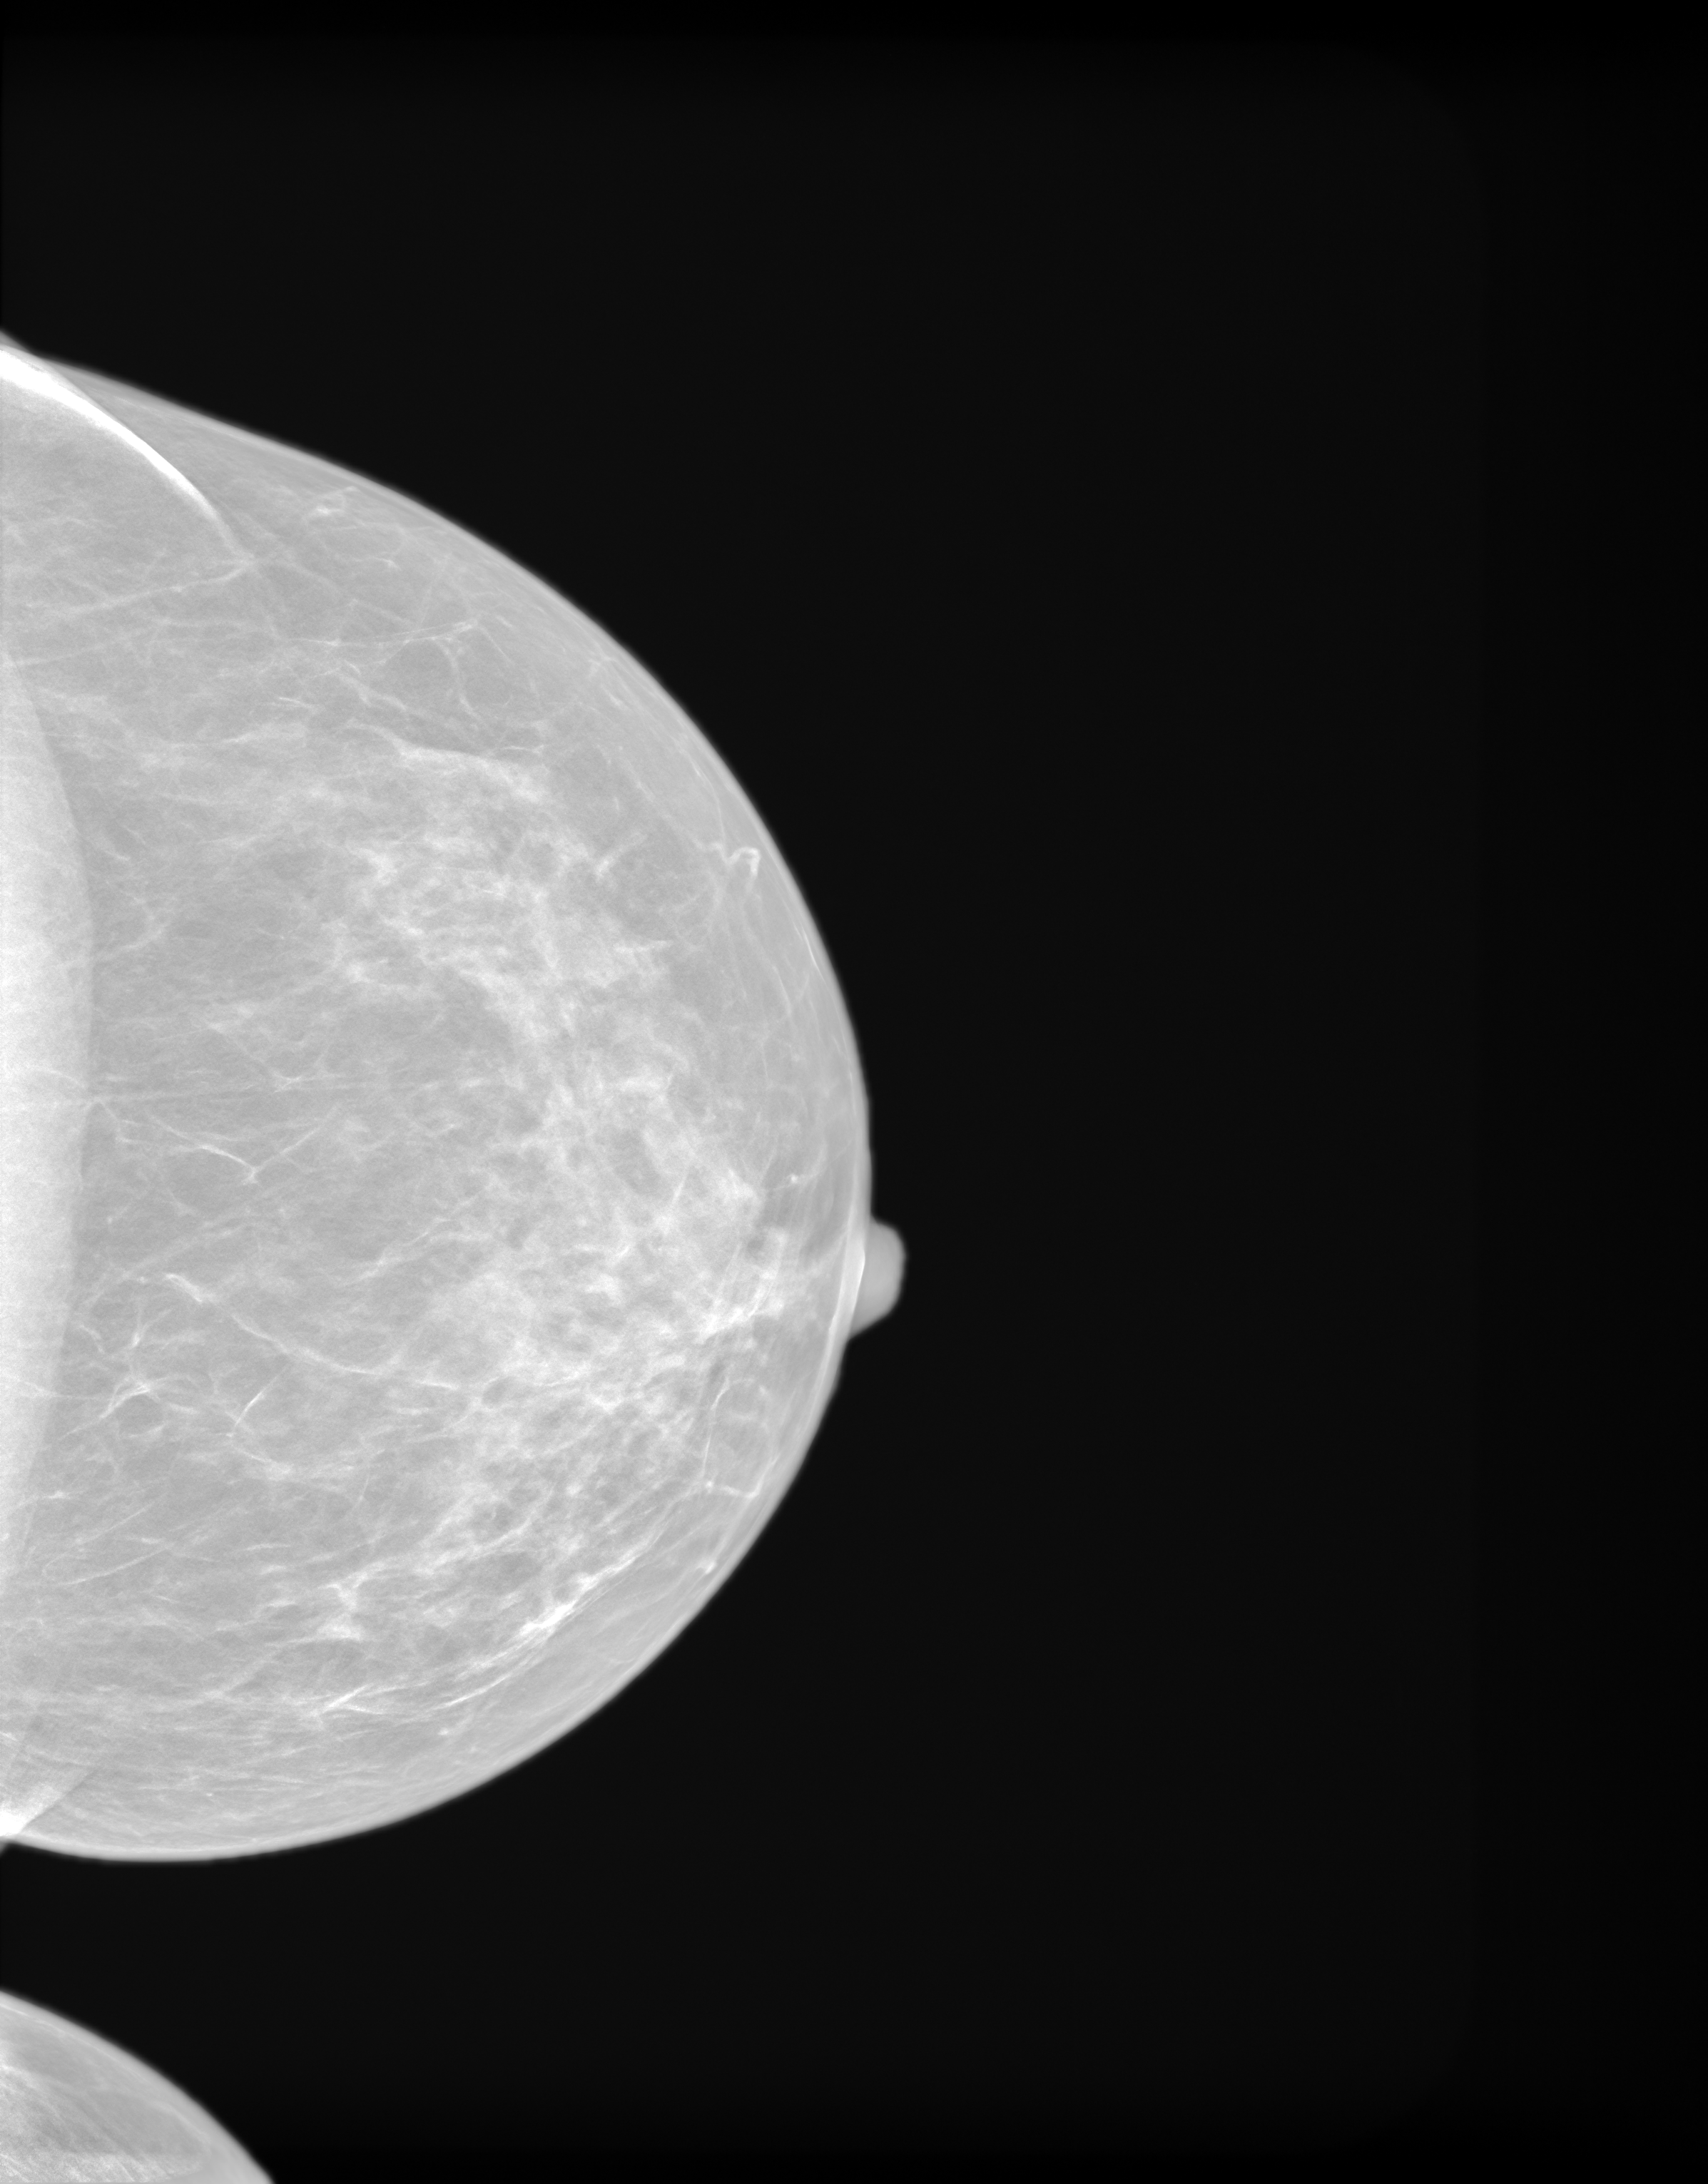
Annual screening mammography examination. Patient: female, 54 years.
Image type: synthesized 2-D view from tomosynthesis. Breast: left. Projection: craniocaudal (CC) view.